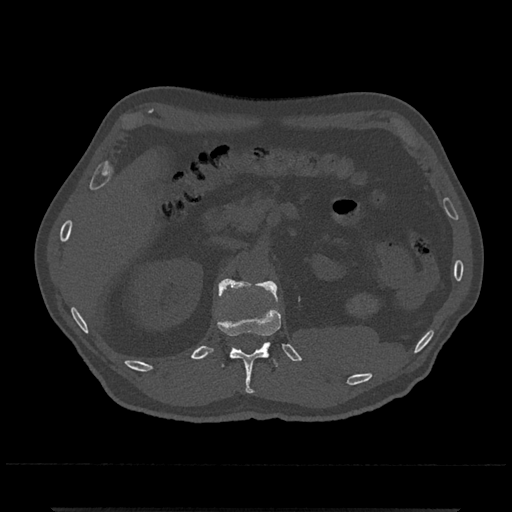
CT including the spine, one axial slice. Reconstruction kernel Br40s/3. 120 kVp. Bone window (W 1800 / L 400 HU). 0.5 mm slice thickness. 512 × 512 image matrix, field of view 393 × 393 mm. Male patient, age 67 years. From the clinical record (not read from this slice): primary cancer: prostate.
Annotated regions visible in this slice (semi-automatic segmentation, software-assisted and operator-edited):
- L1 vertebra: bounding box (x1, y1, x2, y2) in pixels: (218, 279, 278, 301)
- T12 vertebra: (218, 309, 282, 394)